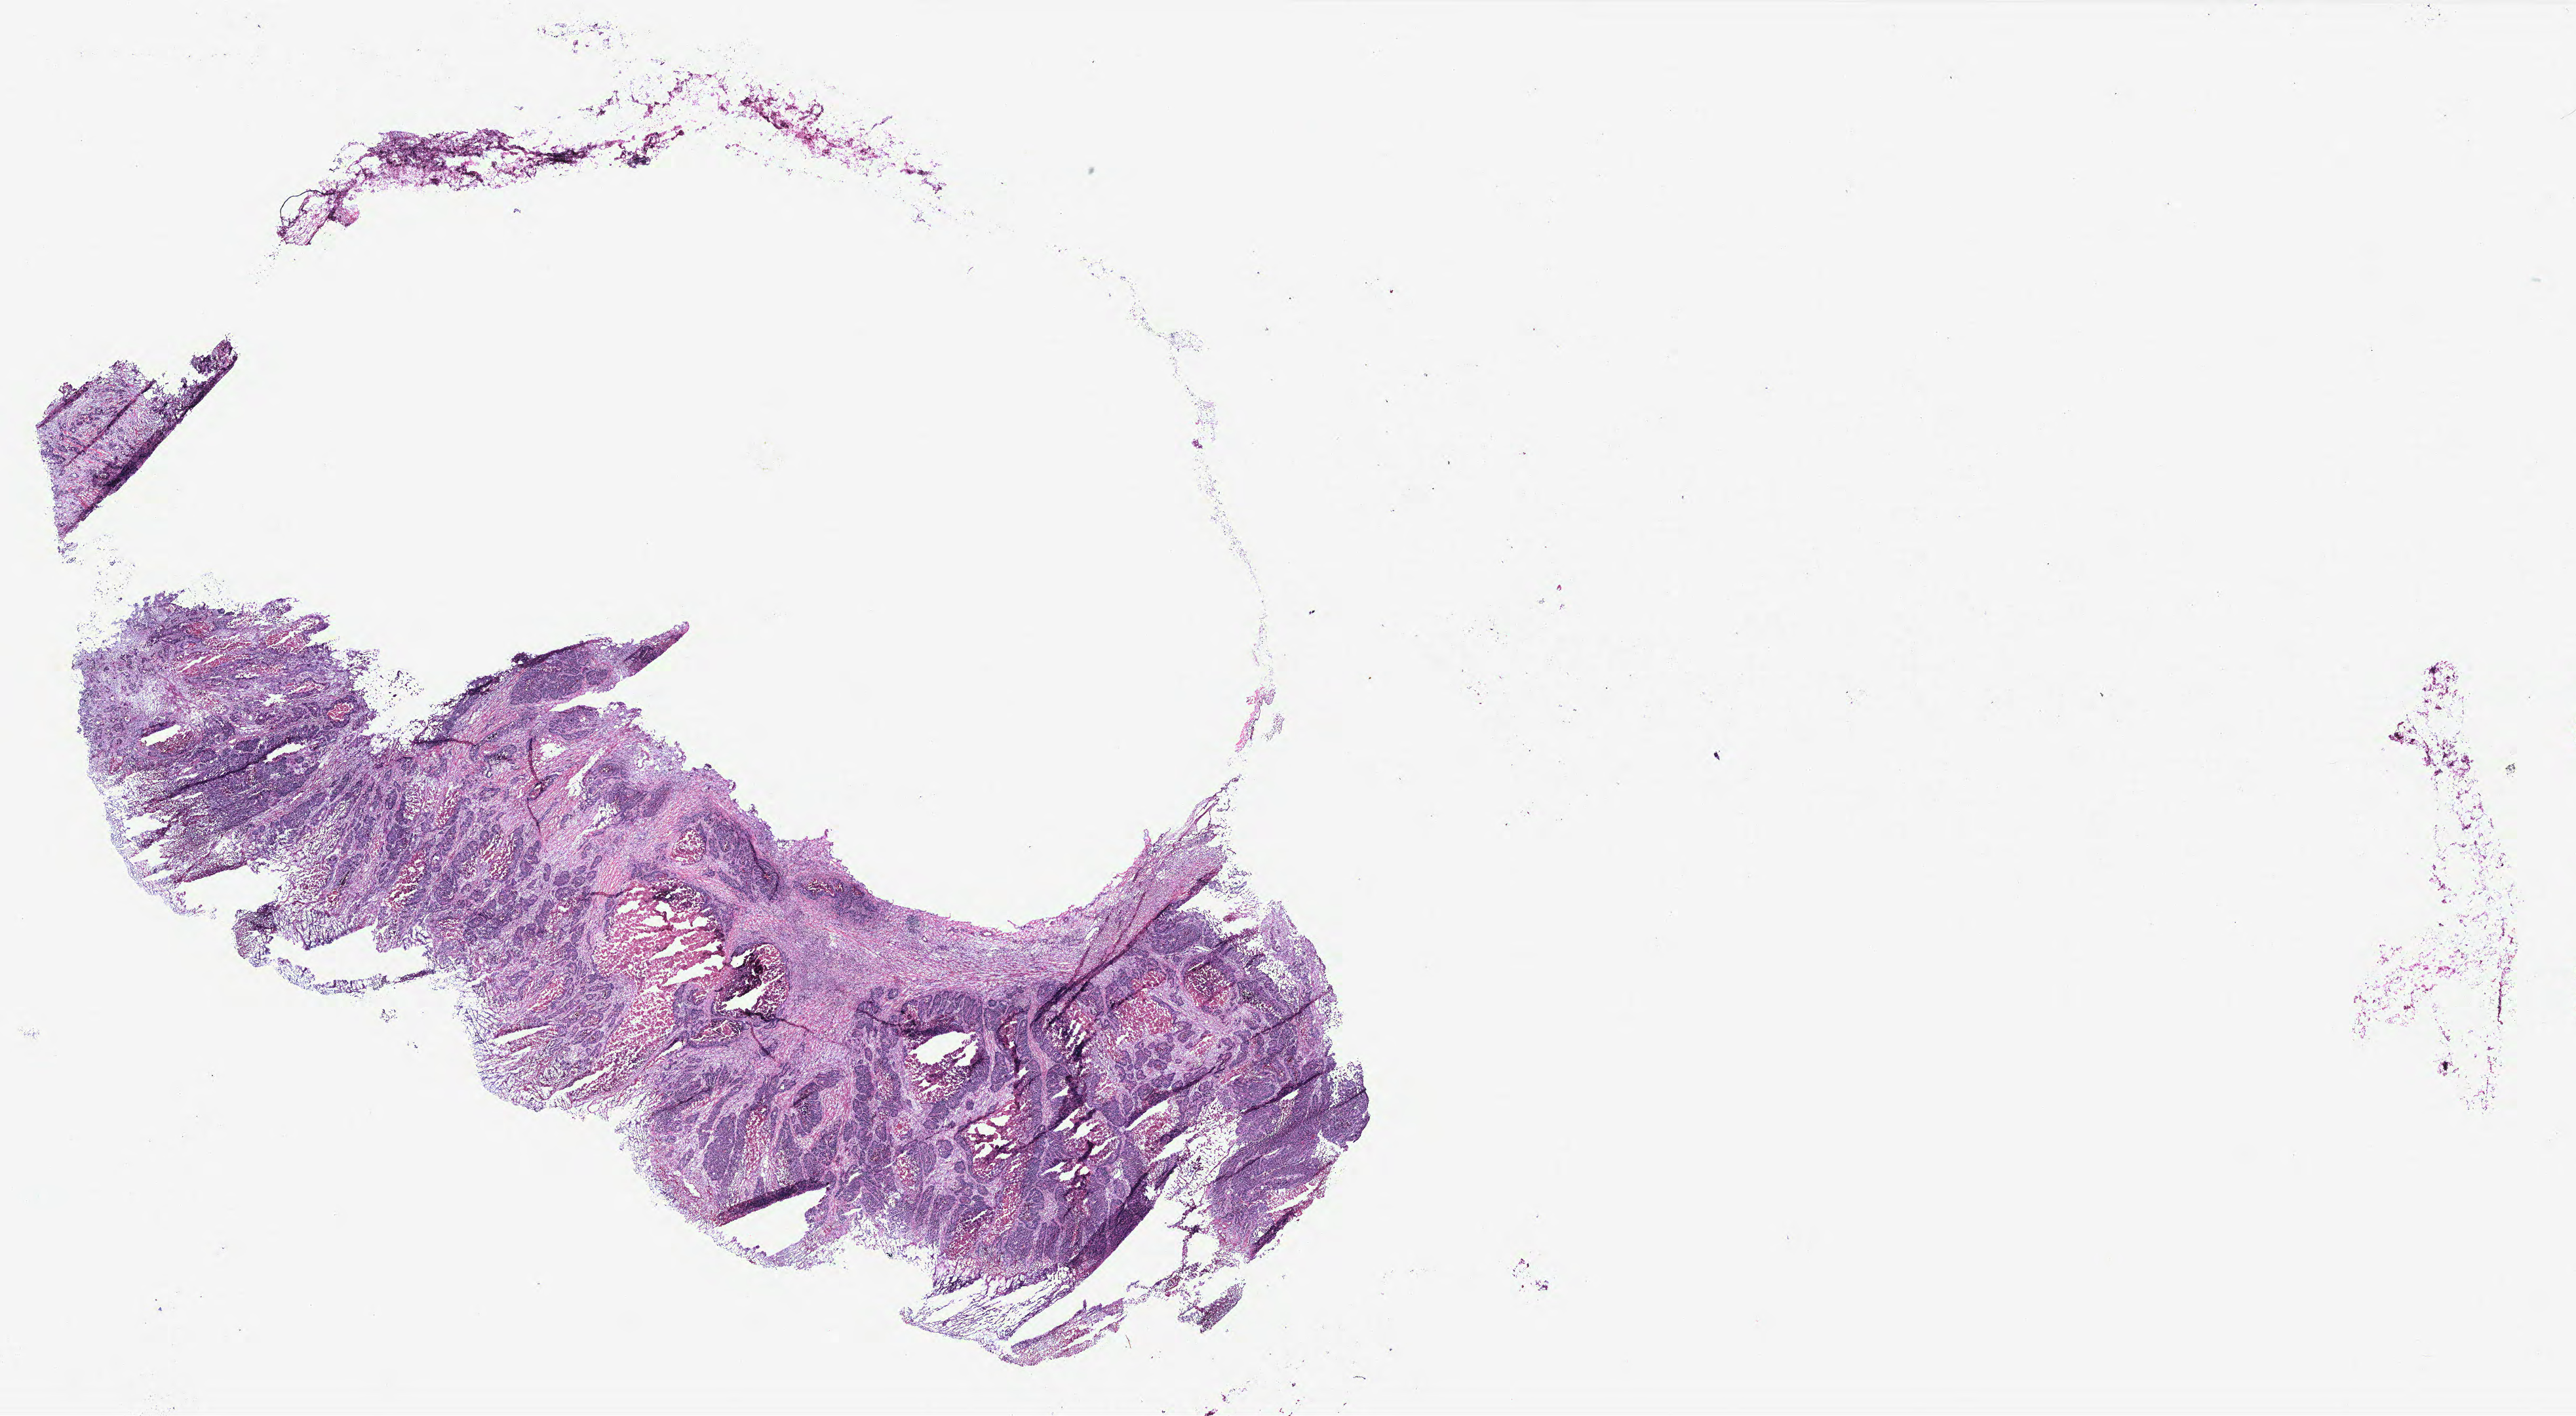
Whole-slide histology image, H&E — a low-resolution overview of the entire scanned area, about 31.5 x 17.3 mm; colon, tumour tissue. Female, 74 y/o.
AJCC pathologic stage: IVA. Diagnosis: Adenocarcinoma, NOS. Primary tumour site (as recorded): colon.